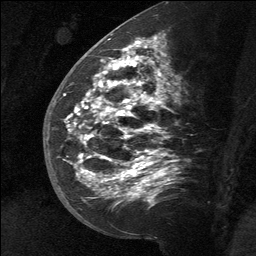
Breast MRI (dynamic contrast-enhanced), one sagittal slice. Position 33 of 64 along the scan axis. Dynamic contrast-enhanced study with each time point stored as its own series, time point 2 of 3 at this slice position (early post-contrast, ordered by acquisition time). 1.5 T. TE 4.8 ms, TR 27 ms. 2 mm slice thickness. 256 × 256 image matrix, field of view 180 × 180 mm. Female patient, age 39 years. Case-level facts recorded for this patient, not image findings: setting: breast cancer imaged before/during neoadjuvant chemotherapy; receptor status: HER2-positive.
Outlined on this slice (semi-automatic segmentation, software-assisted and operator-edited):
- analysis volume of interest (the breast-tissue region the enhancement analysis was run in; not a lesion): bounding box (x1, y1, x2, y2) in pixels: (58, 40, 169, 217)
- tumour enhancement mask (voxels above the 90 % enhancement threshold inside the analysis volume of interest): (67, 40, 155, 197)